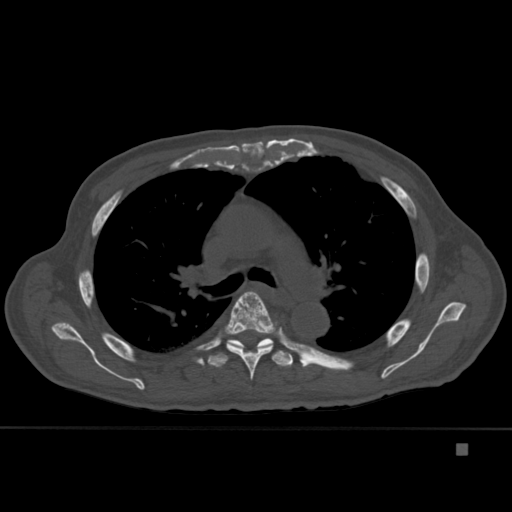
CT including the spine, one axial slice. Position 304 of 451 along the scan axis. Bone window (W 1800 / L 400 HU). 1.5 mm slice thickness. 512 × 512 image matrix, field of view 378 × 378 mm. Patient: male, 75 years. Case-level facts recorded for this patient, not image findings: primary cancer: prostate.
Structures marked on this image (semi-automatically segmented with operator editing):
- T5 vertebra: bounding box [x1, y1, x2, y2] px = [224, 291, 278, 380]
- T6 vertebra: [208, 338, 293, 367]